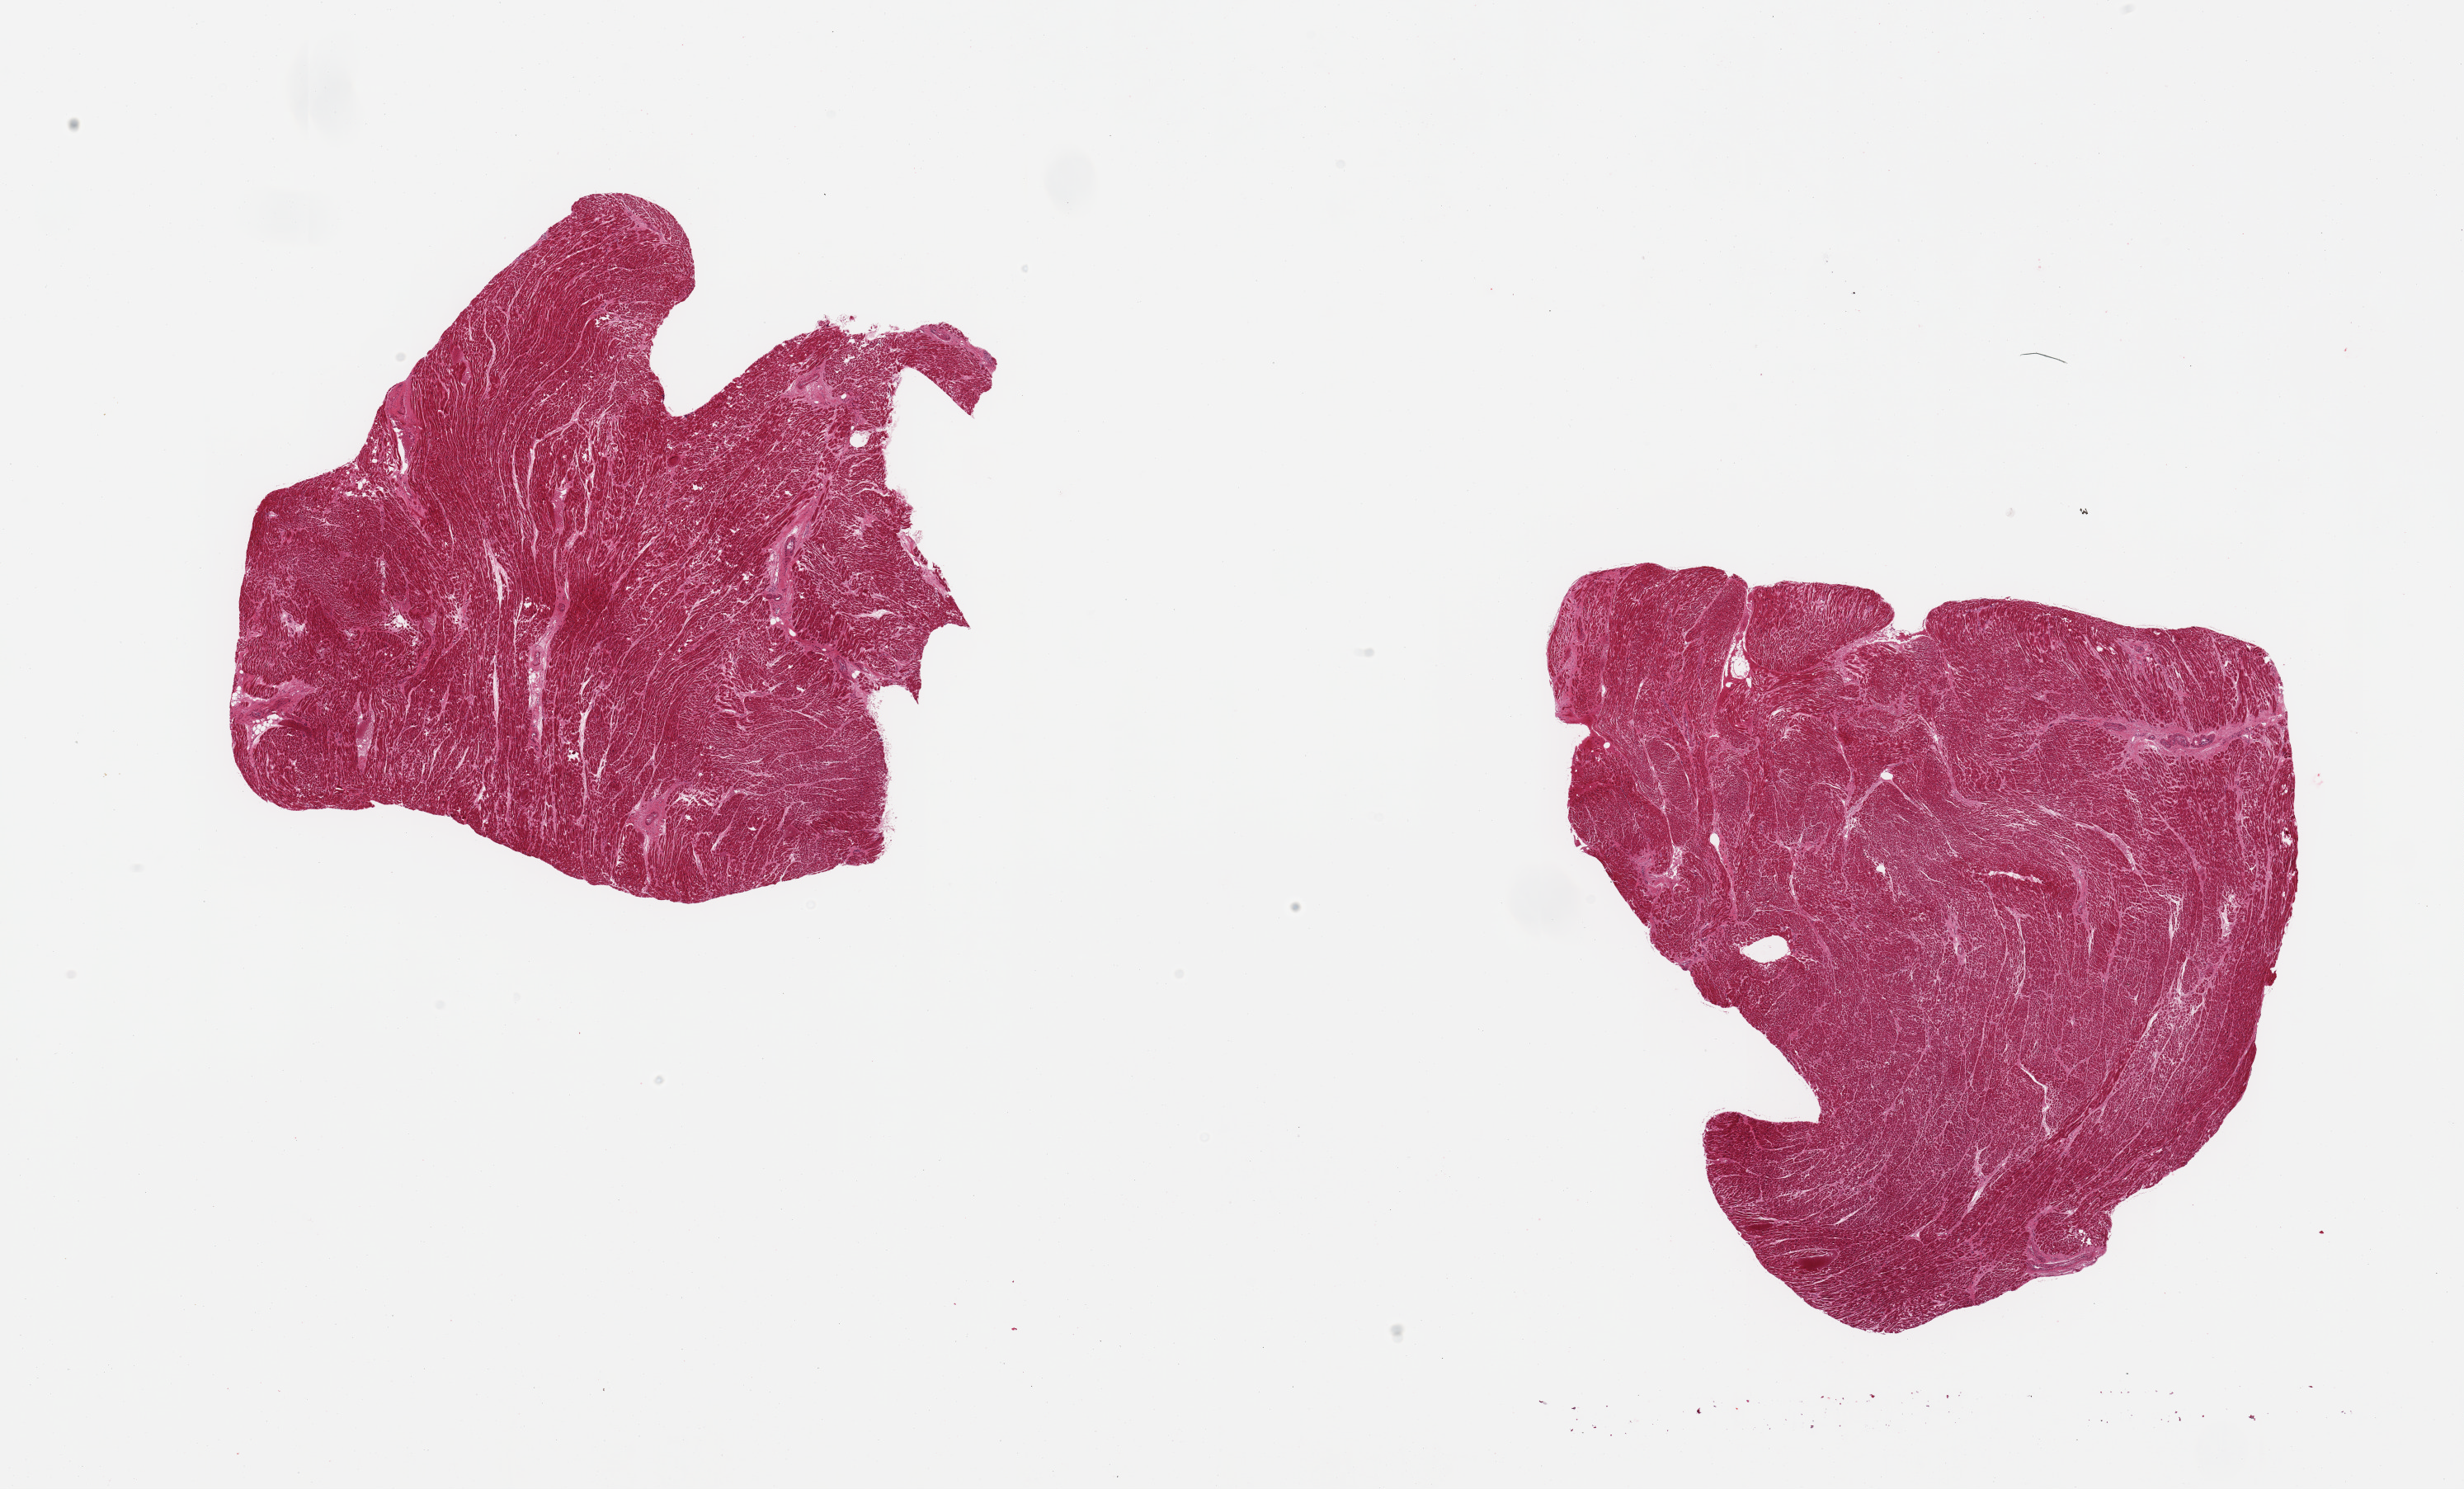
Digitized haematoxylin and eosin-stained section, whole scanned area (about 23.6 x 14.3 mm) shown as a low-resolution overview. PAXgene-fixed, paraffin-embedded tissue. Sampled site (target tissue): heart. Donor tissue sample. Donor sex: female.
Review note (as recorded): 2 pieces; scattered contraction bands and enlarged nuclei.